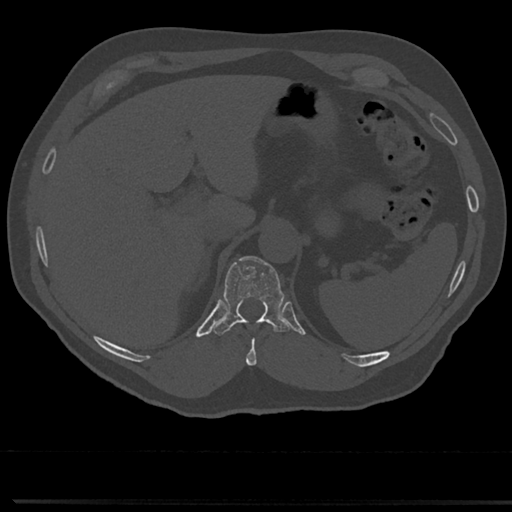
CT including the spine, one axial slice; reconstruction kernel Br40s/3; bone window (W 1800 / L 400 HU); 0.5 mm slice thickness; 512 × 512 image matrix, field of view 355 × 355 mm. Patient: male, 61 years. Case-level facts recorded for this patient, not image findings: primary cancer: prostate.
Structures marked on this image (semi-automatic segmentation, software-assisted and operator-edited):
- T10 vertebra: box from (x=246, y=322) to (x=270, y=366) px
- T11 vertebra: (x=217, y=256)–(x=287, y=335)